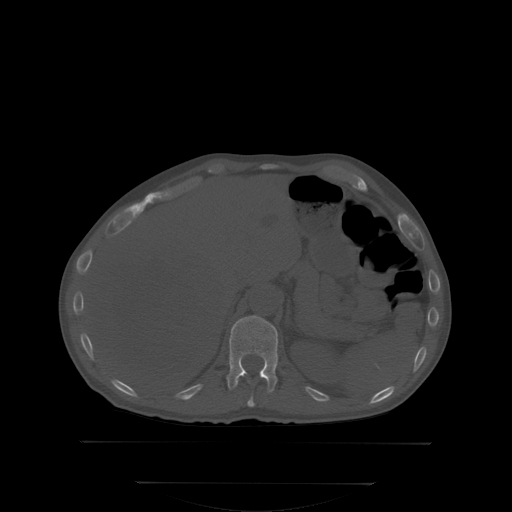
CT including the spine, one axial slice. Slice 171 of 350 in the series (ordered by position). Bone window (W 1800 / L 400 HU). 2.5 mm slice thickness. 512 × 512 image matrix, field of view 500 × 500 mm. Patient: male, 58 years. Case-level facts recorded for this patient, not image findings: primary cancer: prostate; vertebrae with lytic lesions (as recorded): L1.
Annotated regions visible in this slice (semi-automatically segmented with operator editing):
- T11 vertebra: box from (x=248, y=396) to (x=255, y=406) px
- T12 vertebra: (x=227, y=315)–(x=278, y=392)